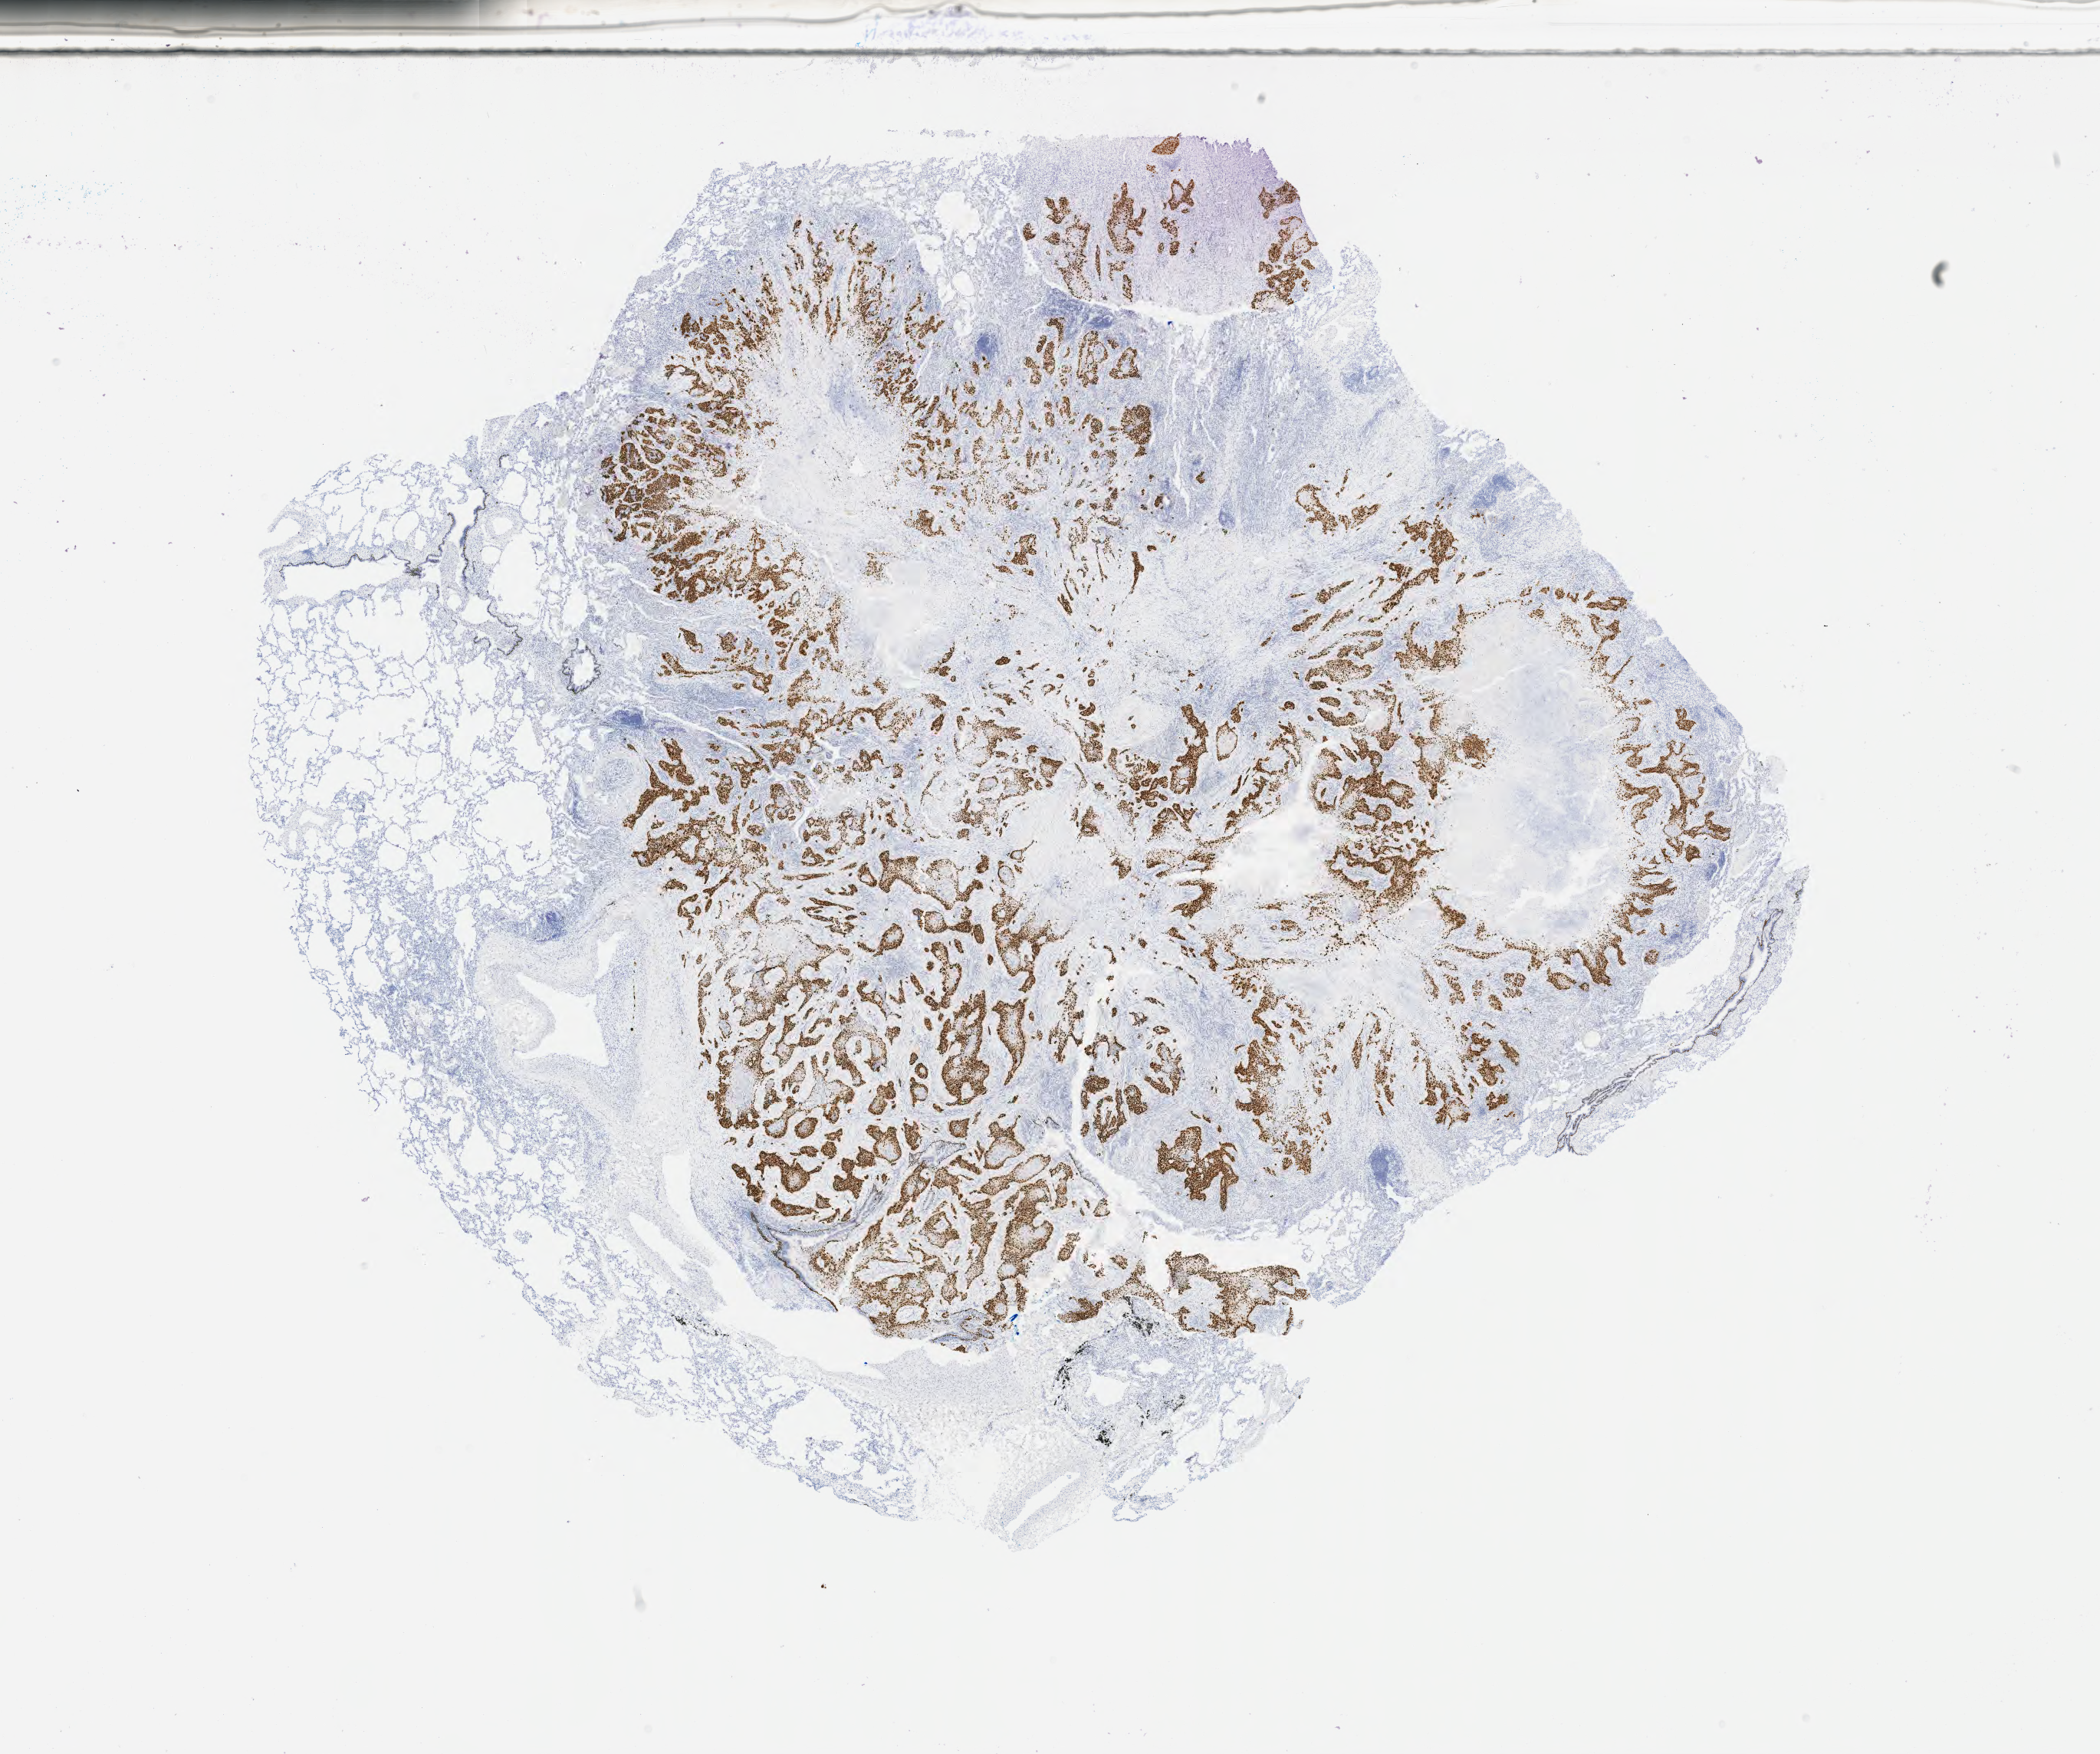
Whole-slide image, immunohistochemical stain for p40 — a low-resolution overview of the entire scanned area, about 22.1 x 18.5 mm. Patient sex: male.
Specimen: tumor tissue; anatomic site: lower respiratory tract.